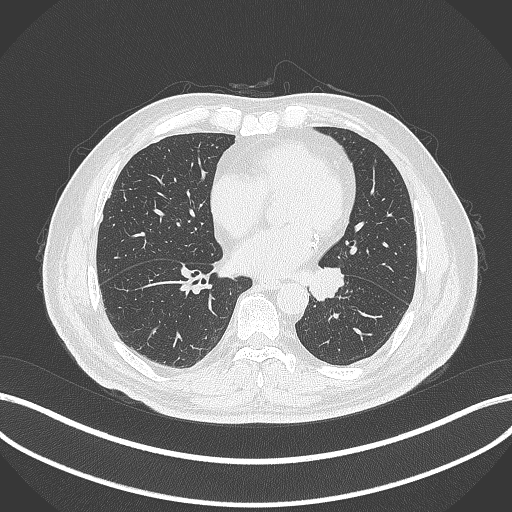
Chest CT, one axial slice; slice 118 of 312 in the series (ordered by position); reconstruction kernel B70f; 120 kVp; lung window (W 1500 / L -600 HU); 1 mm slice thickness; 512 × 512 image matrix. Male patient, age 71 years. From the clinical record (not read from this slice): clinical TNM (as recorded): T1b N0 M0.
Structures marked on this image (bounding box drawn by a radiologist):
- lung tumour (recorded histology: squamous cell carcinoma): bounding box [x1, y1, x2, y2] px = [307, 265, 347, 303]